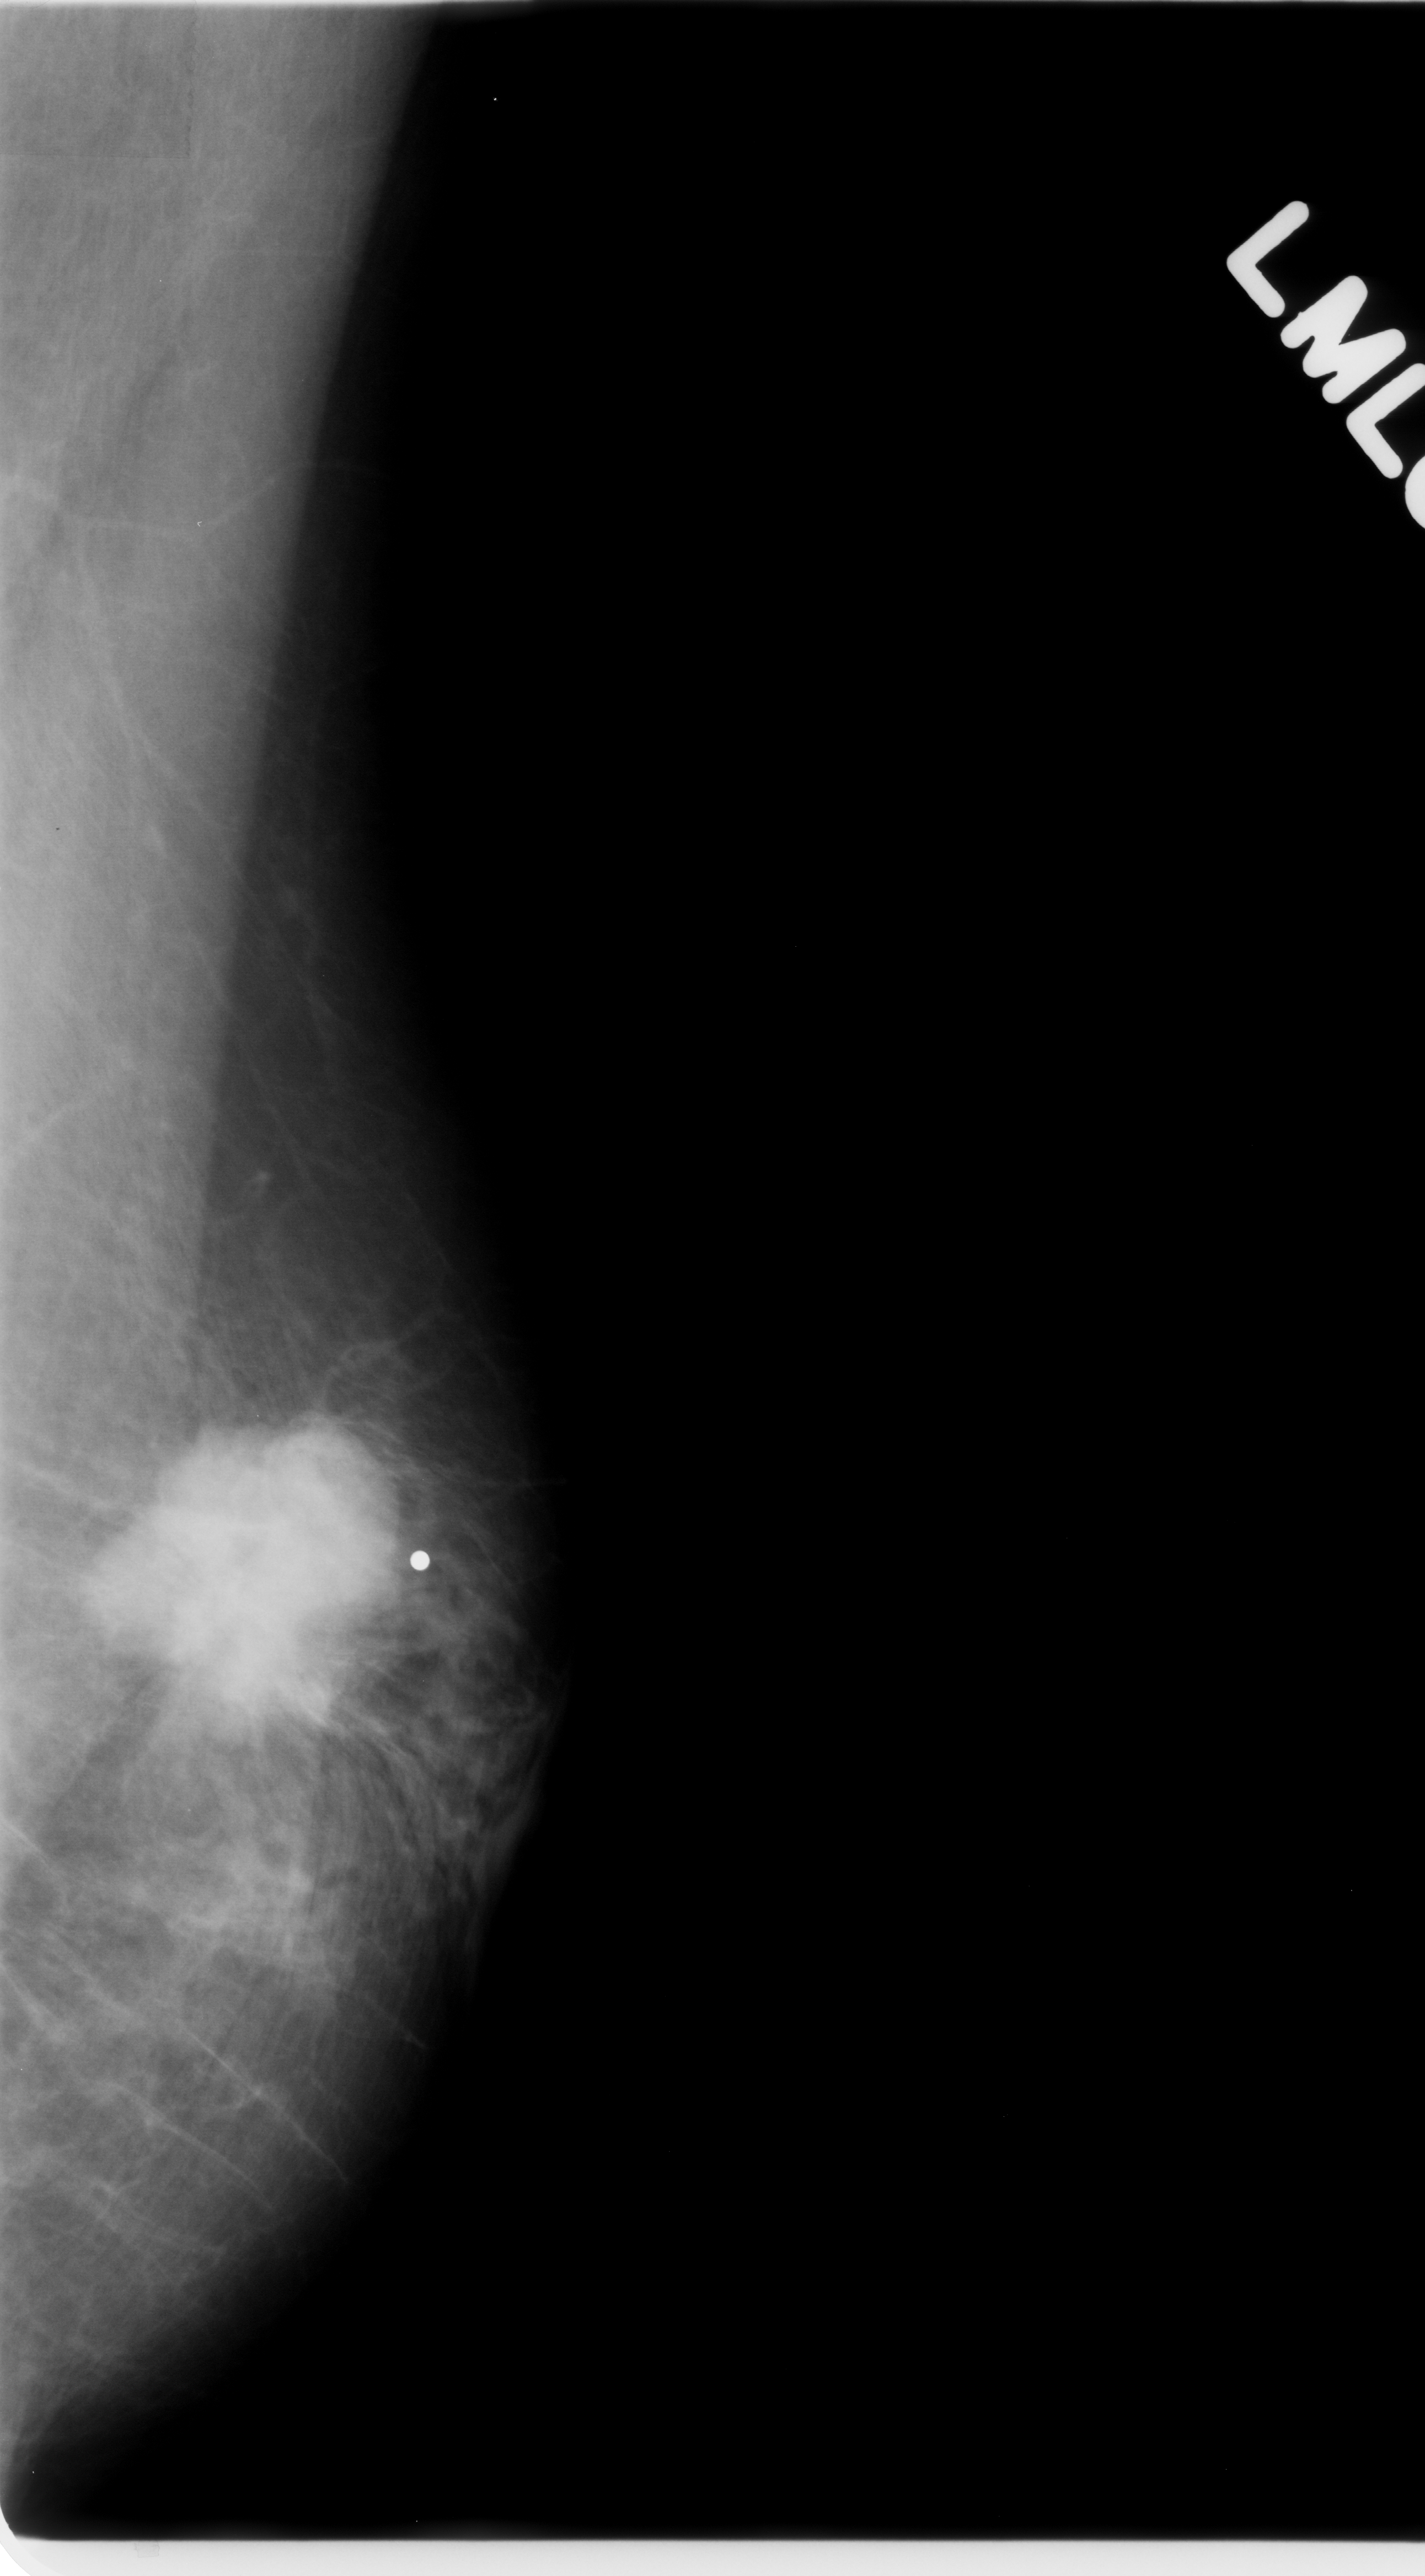
Digitized screen-film mammogram; left breast; mediolateral oblique (MLO) view; breast composition: scattered fibroglandular densities (BI-RADS density category 2 of 4).
Mass, shape irregular, margins spiculated; BI-RADS assessment category 5; pathology result (as recorded, not read from the image): malignant.